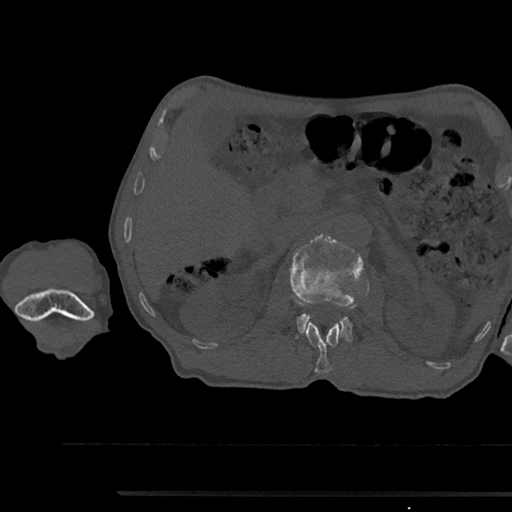
CT including the spine, one axial slice. Position 604 of 797 along the scan axis. 120 kVp. Bone window (W 1800 / L 400 HU). 0.5 mm slice thickness. 512 × 512 image matrix, field of view 367 × 367 mm. Patient: male, 79 years. From the clinical record (not read from this slice): primary cancer: prostate.
Structures marked on this image (semi-automatic segmentation, software-assisted and operator-edited):
- L1 vertebra: bounding box [x1, y1, x2, y2] px = [305, 322, 340, 373]
- L2 vertebra: [290, 235, 364, 342]